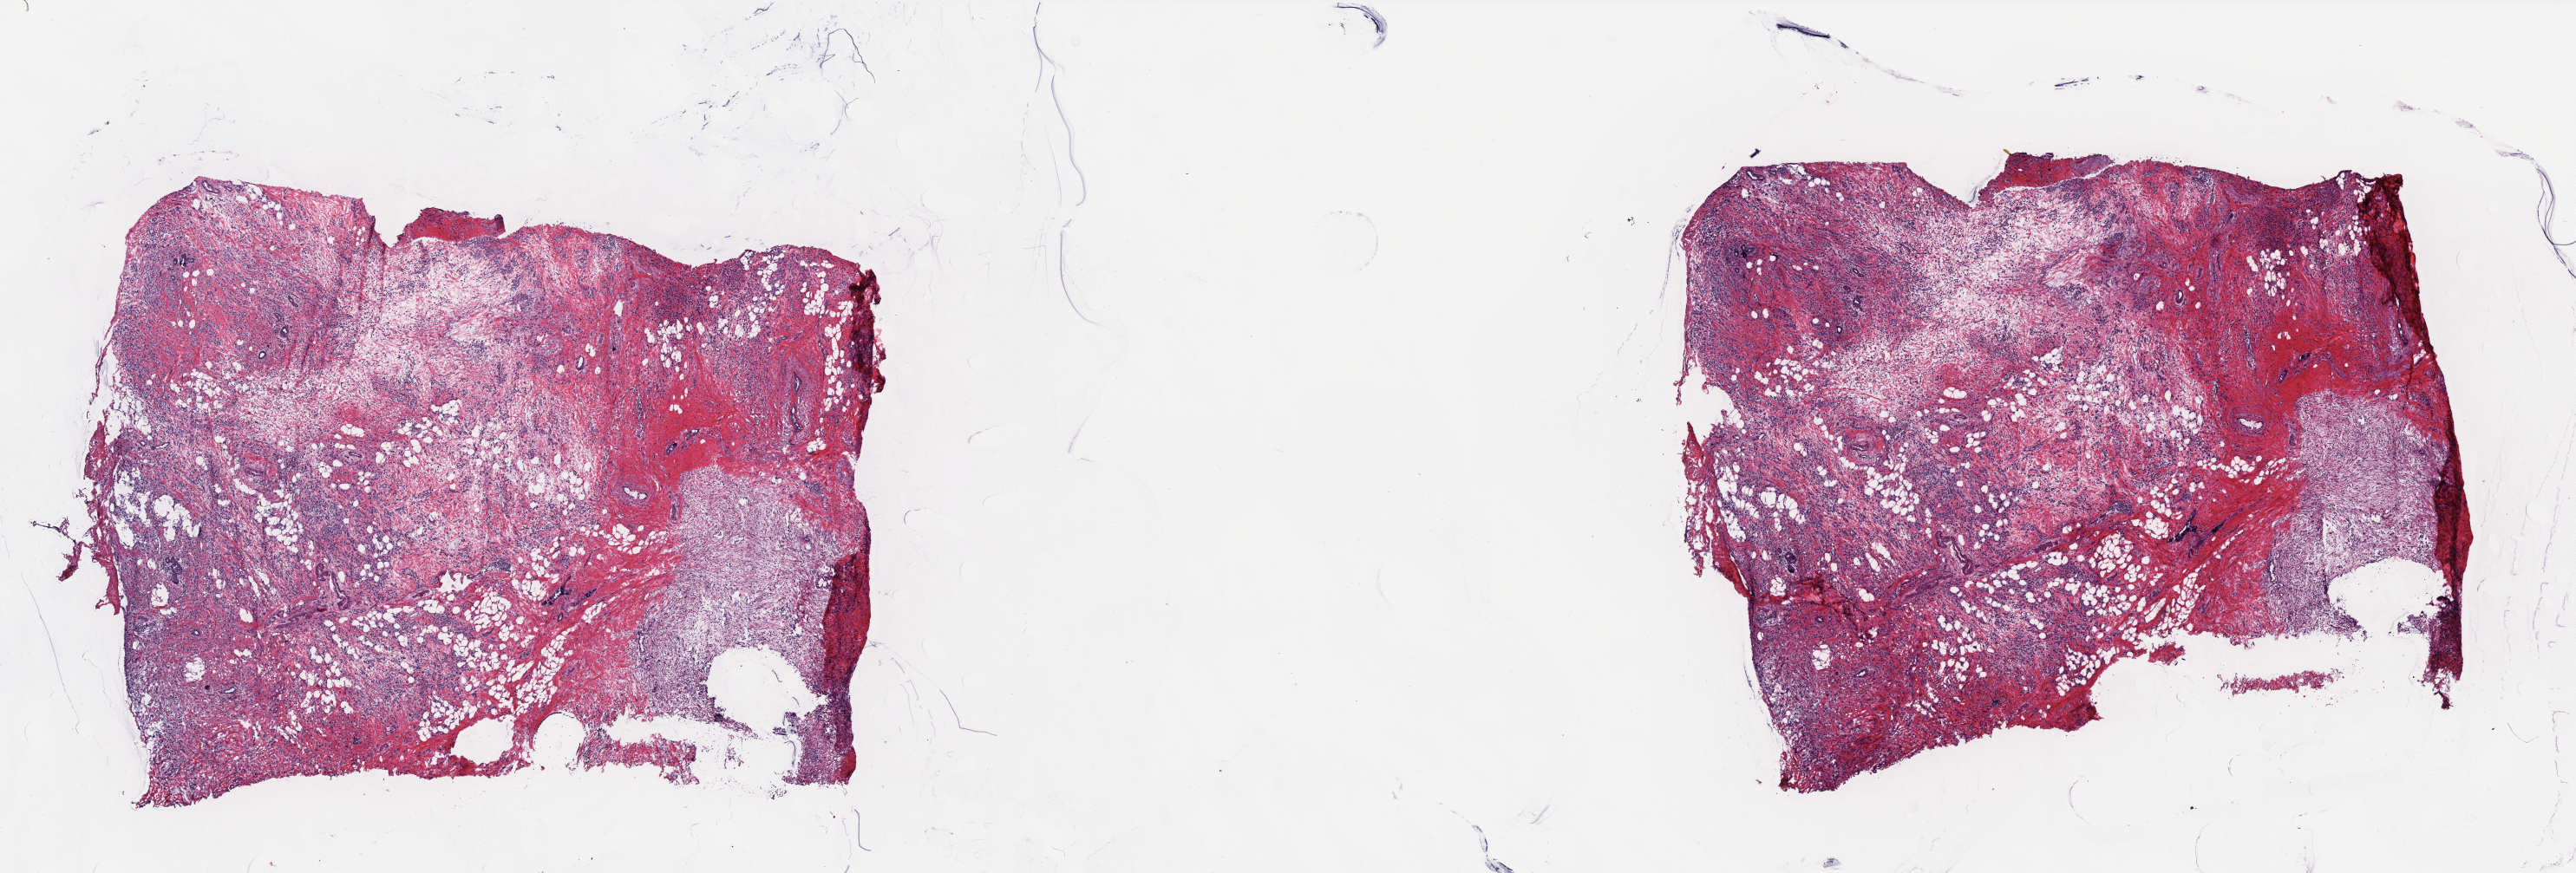
Whole-slide histology image, H&E, shown as a low-resolution overview of the whole scanned area (about 23.8 x 8.1 mm, from a 40x scan); frozen section from the bottom of the tissue portion; breast, primary tumour sample. Female, age 78 years at initial diagnosis. Pathologist review of this section (percent, as recorded): tumour cells 70%, tumour nuclei 80%, normal cells 10%, stromal cells 18%, necrosis 2%. Infiltration values recorded for this section: lymphocyte infiltration 12%, monocyte infiltration 0%, neutrophil infiltration 0%.
Diagnosis: Infiltrating duct and lobular carcinoma. Laterality: right. AJCC pathologic stage: IIA.